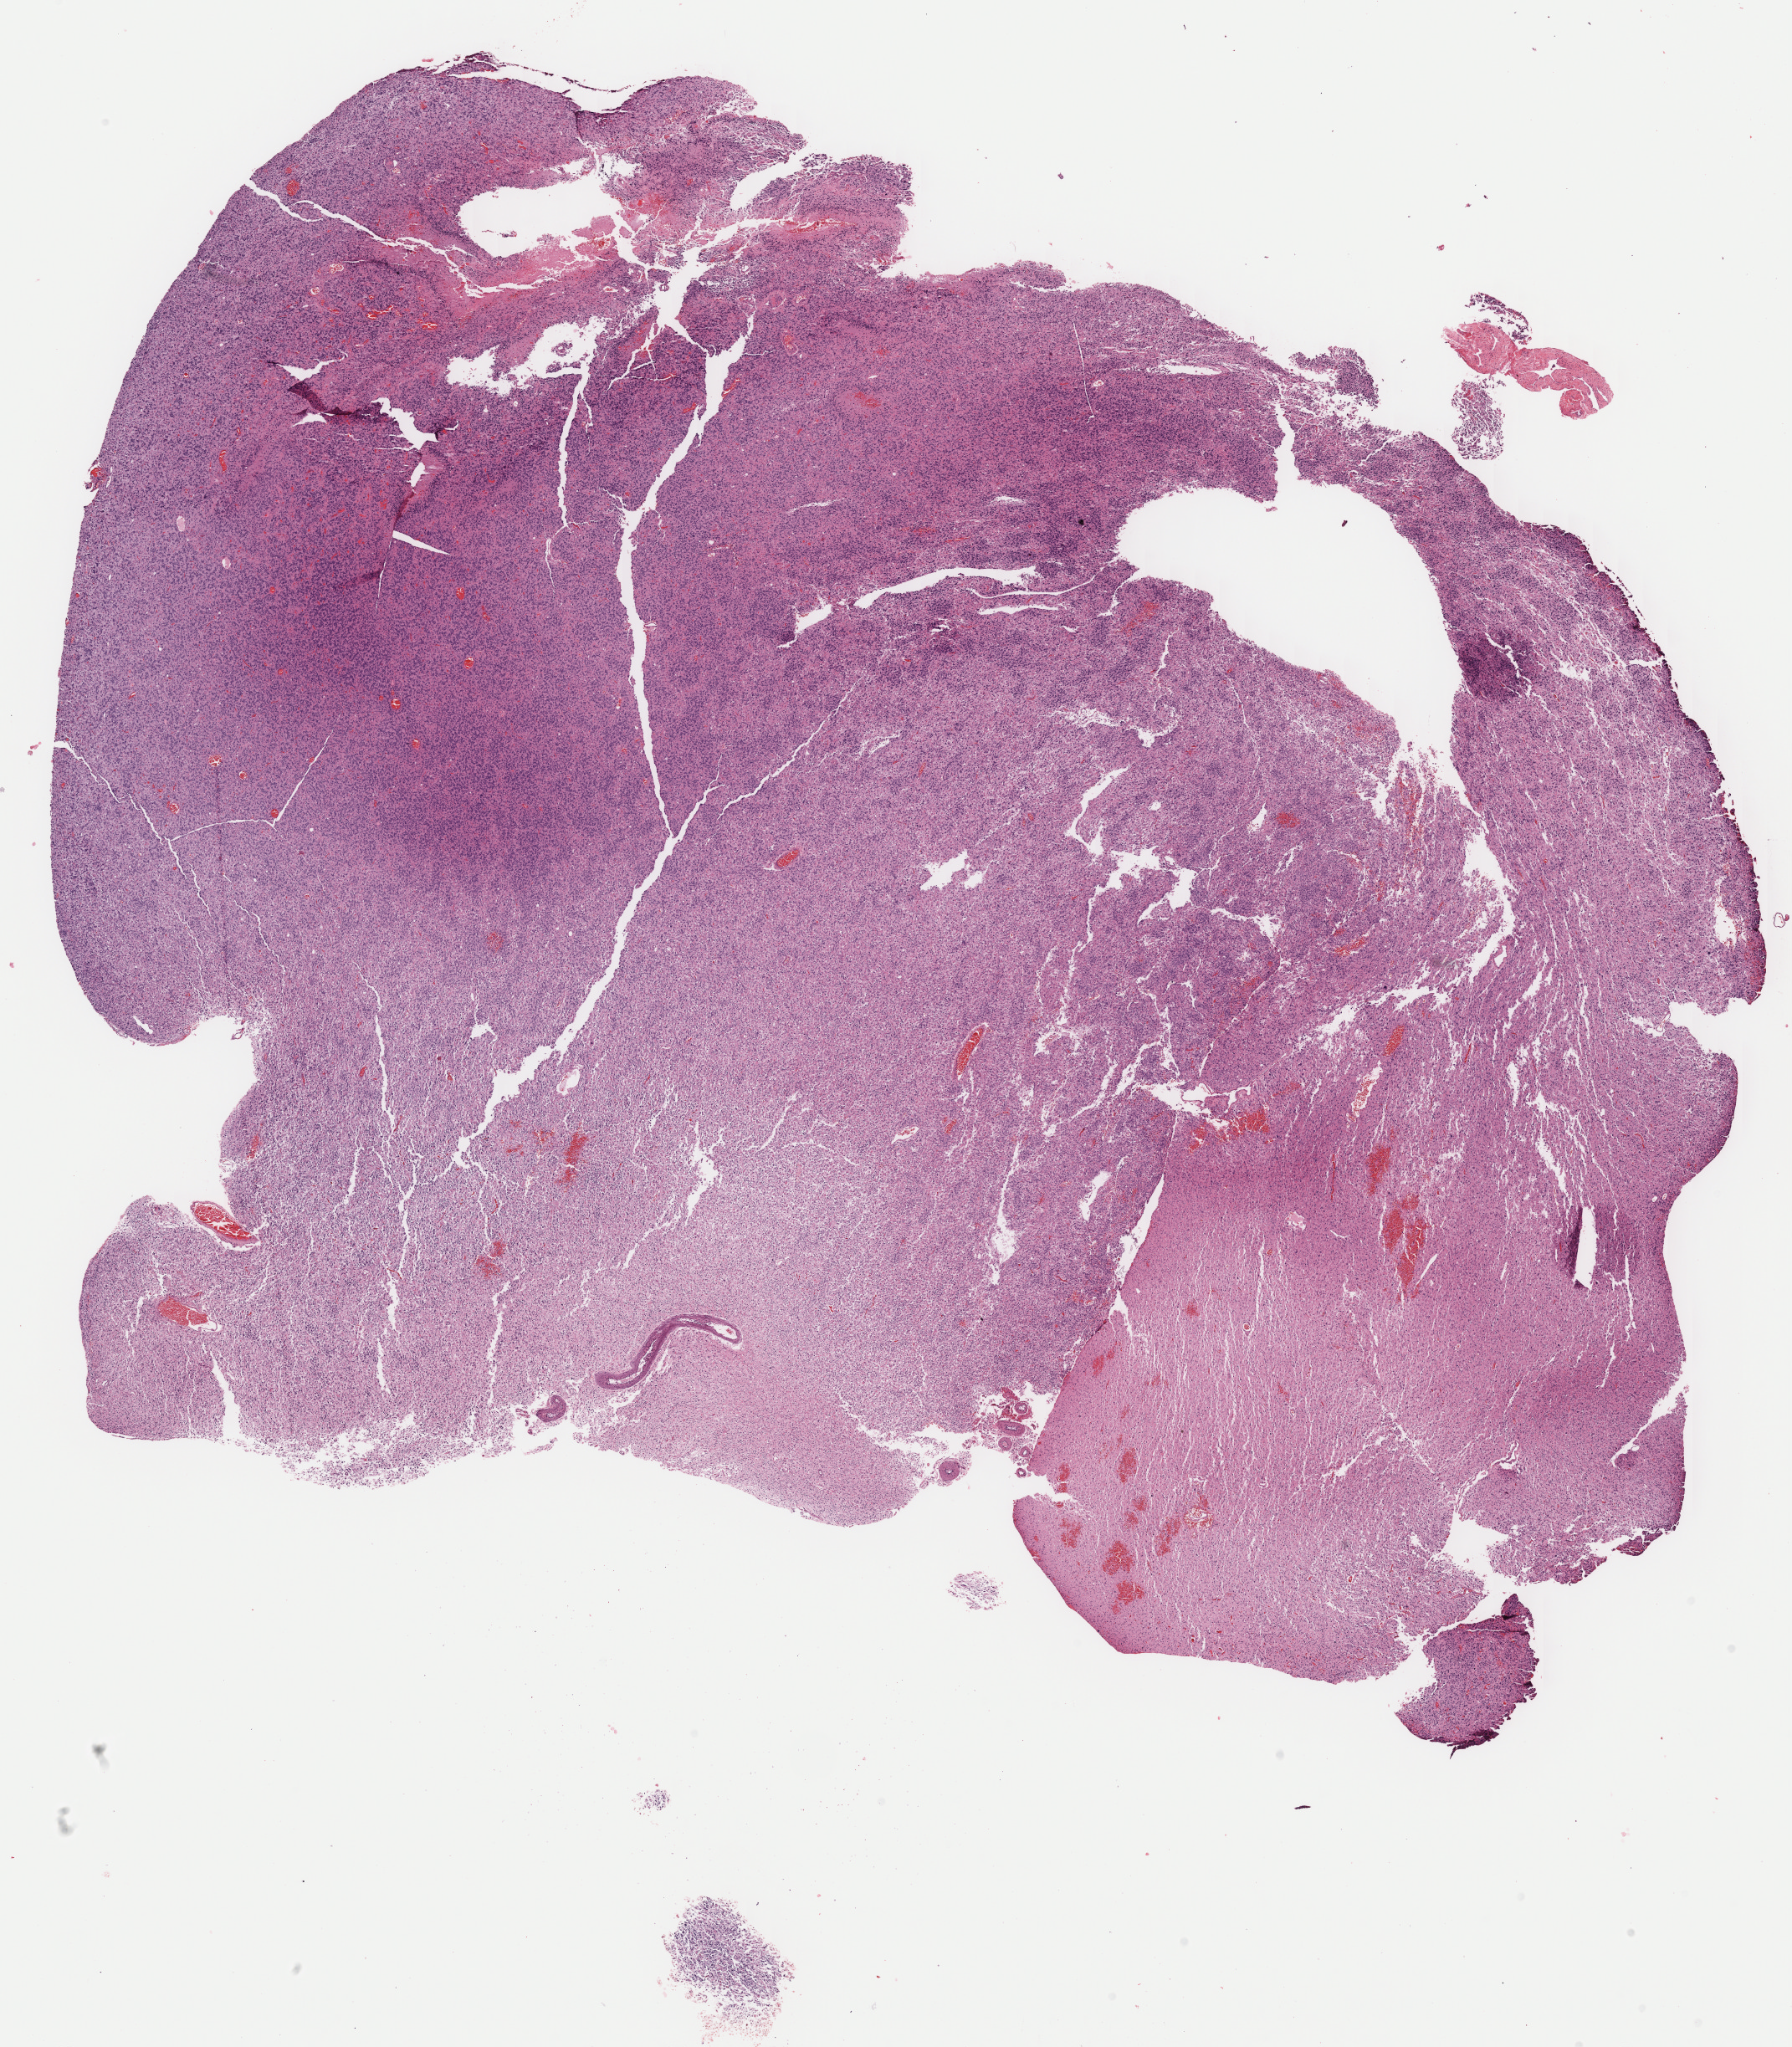
H&E-stained whole-slide image — low-resolution overview of the scanned area, about 16.9 x 19.3 mm (from a 40x scan). Formalin-fixed paraffin-embedded (FFPE) diagnostic section. Primary tumour sample from the brain. Male, age 21 years at initial diagnosis.
Pathologic diagnosis: Glioblastoma.